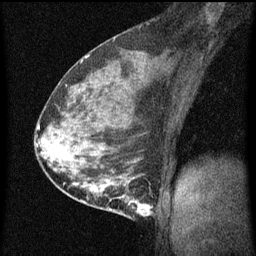
Breast MRI (dynamic contrast-enhanced), one sagittal slice. Slice 34 of 60 in the series (ordered by position). Dynamic contrast-enhanced series, image 2 of 3 at this slice position (ordered by acquisition). 1.5 T. TE 4.2 ms, TR 8 ms. 2 mm slice thickness. 256 × 256 image matrix. Patient: female, 35 years.
Outlined on this slice (semi-automatic segmentation, software-assisted and operator-edited):
- analysis volume of interest (the breast-tissue region the enhancement analysis was run in; not a lesion): bounding box (x1, y1, x2, y2) in pixels: (110, 178, 155, 219)
- tumour enhancement mask (voxels above the 70 % enhancement threshold inside the analysis volume of interest): (110, 178, 152, 217)